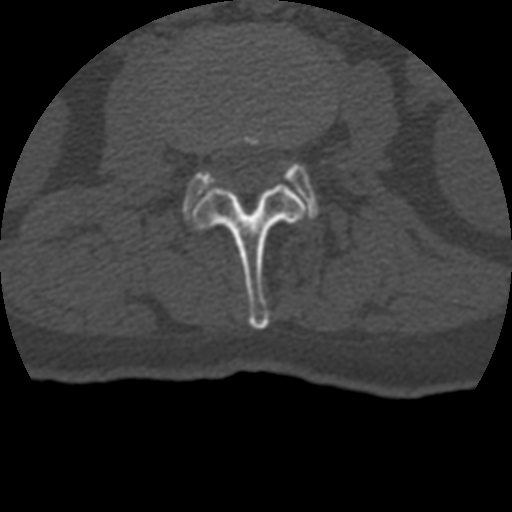
CT including the spine, one axial slice. Position 106 of 399 along the scan axis. Reconstruction kernel STANDARD. 120 kVp. Bone window (W 1800 / L 400 HU). 1.25 mm slice thickness. 512 × 512 image matrix. Patient age 69 years. Case-level facts recorded for this patient, not image findings: primary cancer: prostate.
Structures marked on this image (semi-automatically segmented with operator editing):
- L2 vertebra: box from (x=193, y=135) to (x=305, y=329) px
- L3 vertebra: (x=184, y=163)–(x=317, y=212)